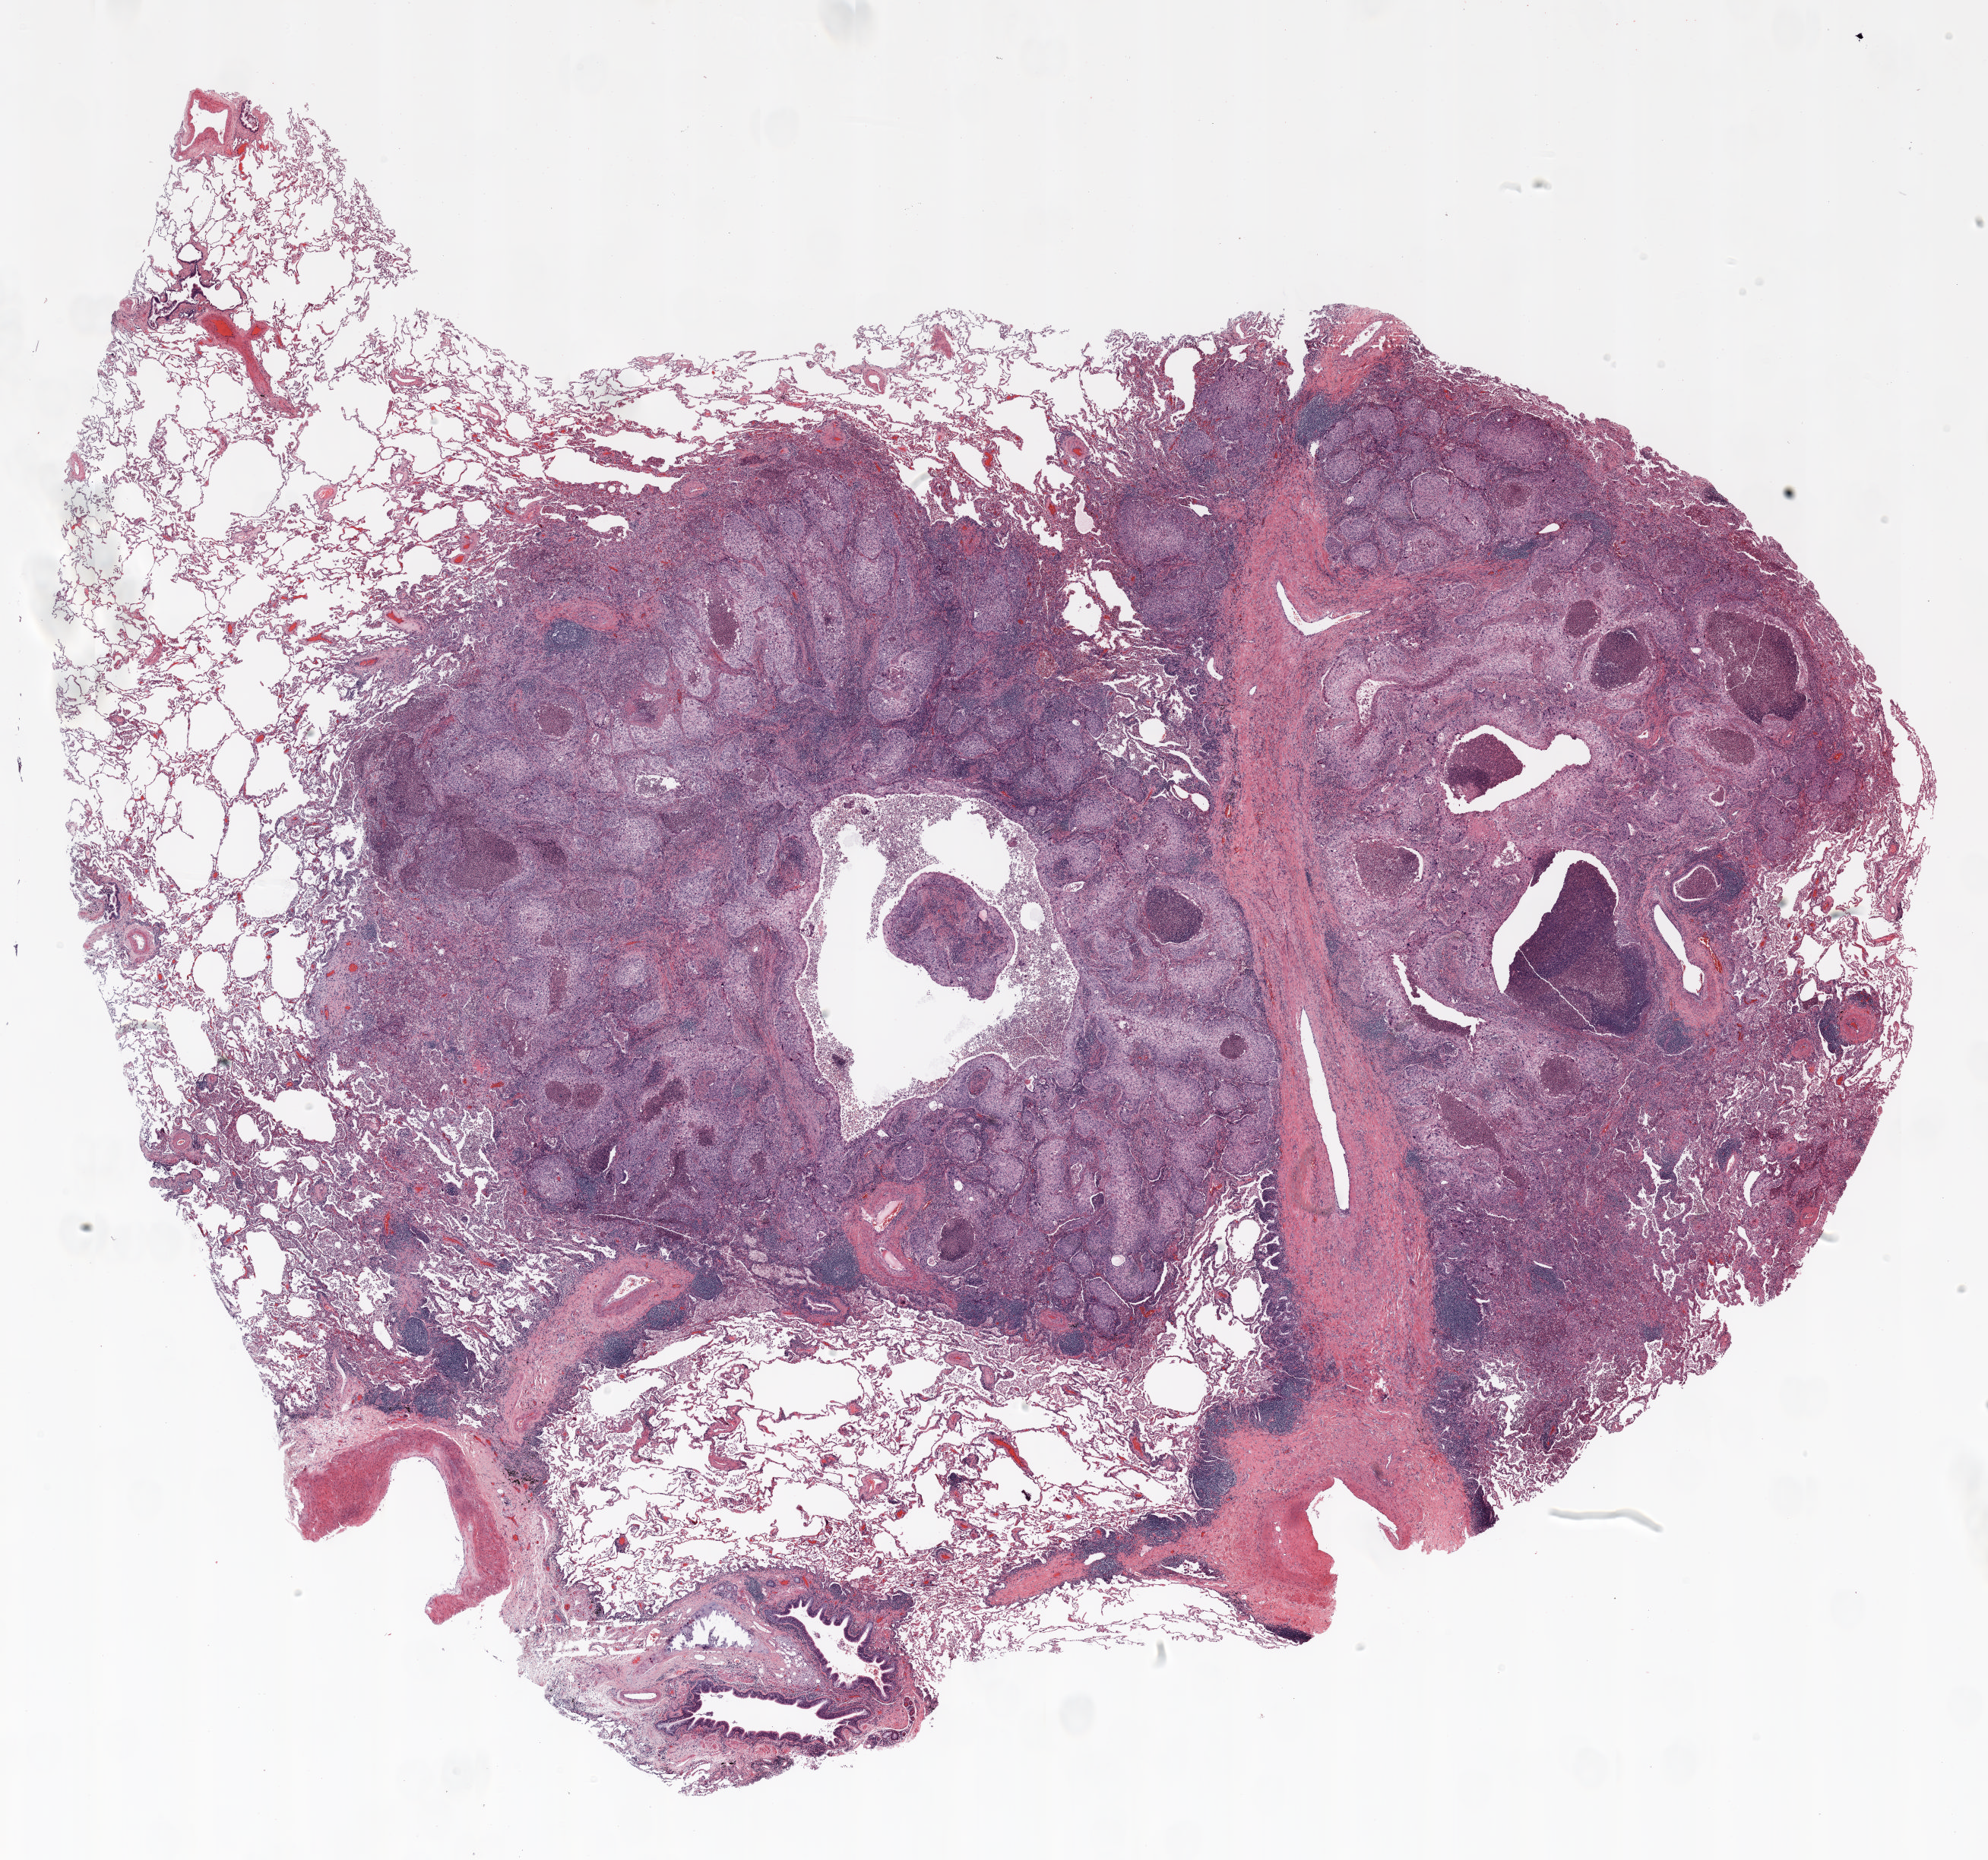
H&E-stained whole-slide image, low-resolution overview of the scanned area, about 21.0 x 19.7 mm (slide scanned at 20x). FFPE section. Lung. Male, age 73 at enrolment. Current smoker at enrolment. Grade: poorly differentiated (G3).
Stage (AJCC 6th edition): IA. Participant's lung-cancer diagnosis: Squamous cell carcinoma, NOS (ICD-O-3 8070/3). Tumour size (pathology): 25 mm. ICD-O-3 topography: lower lobe of lung (C34.3). Primary tumour location (clinical record): left lower lobe.